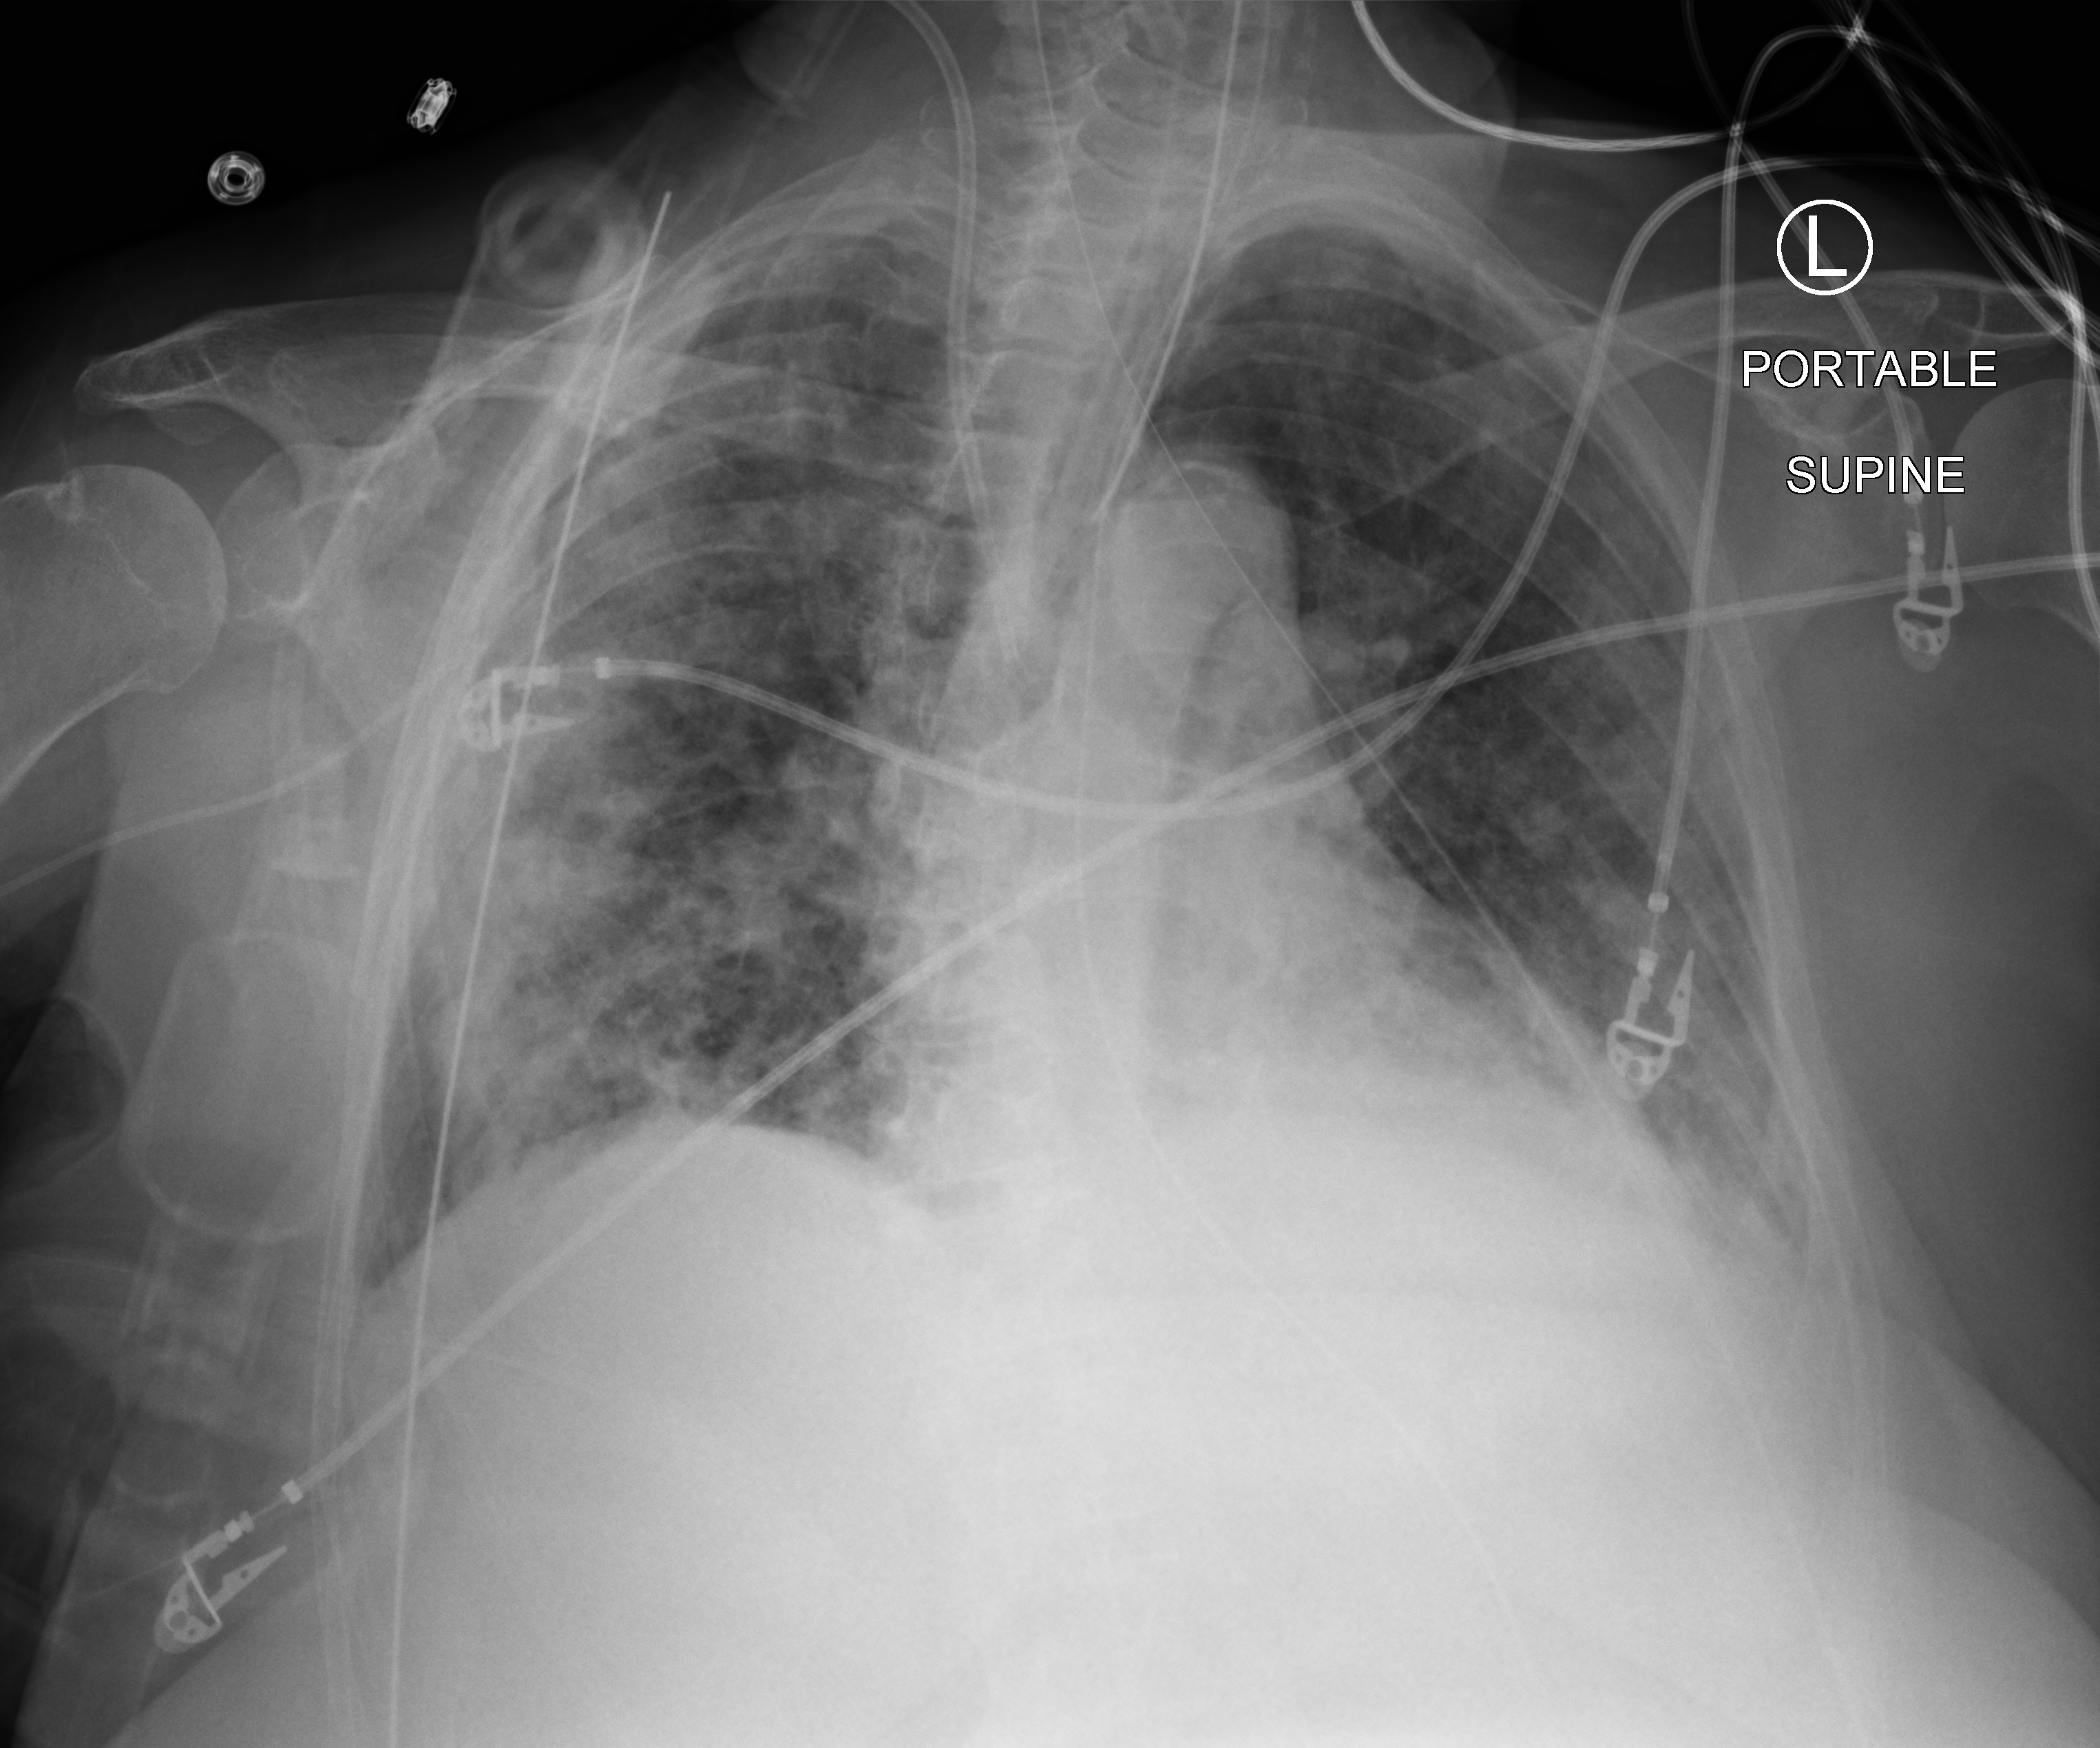
Portable chest radiograph; anteroposterior (AP) projection. Female patient hospitalised with COVID-19, age 75–90 years.
From the hospital-stay record, not from the radiograph (when in the stay this image was taken is not recorded): other chronic lung disease (admission record): no.